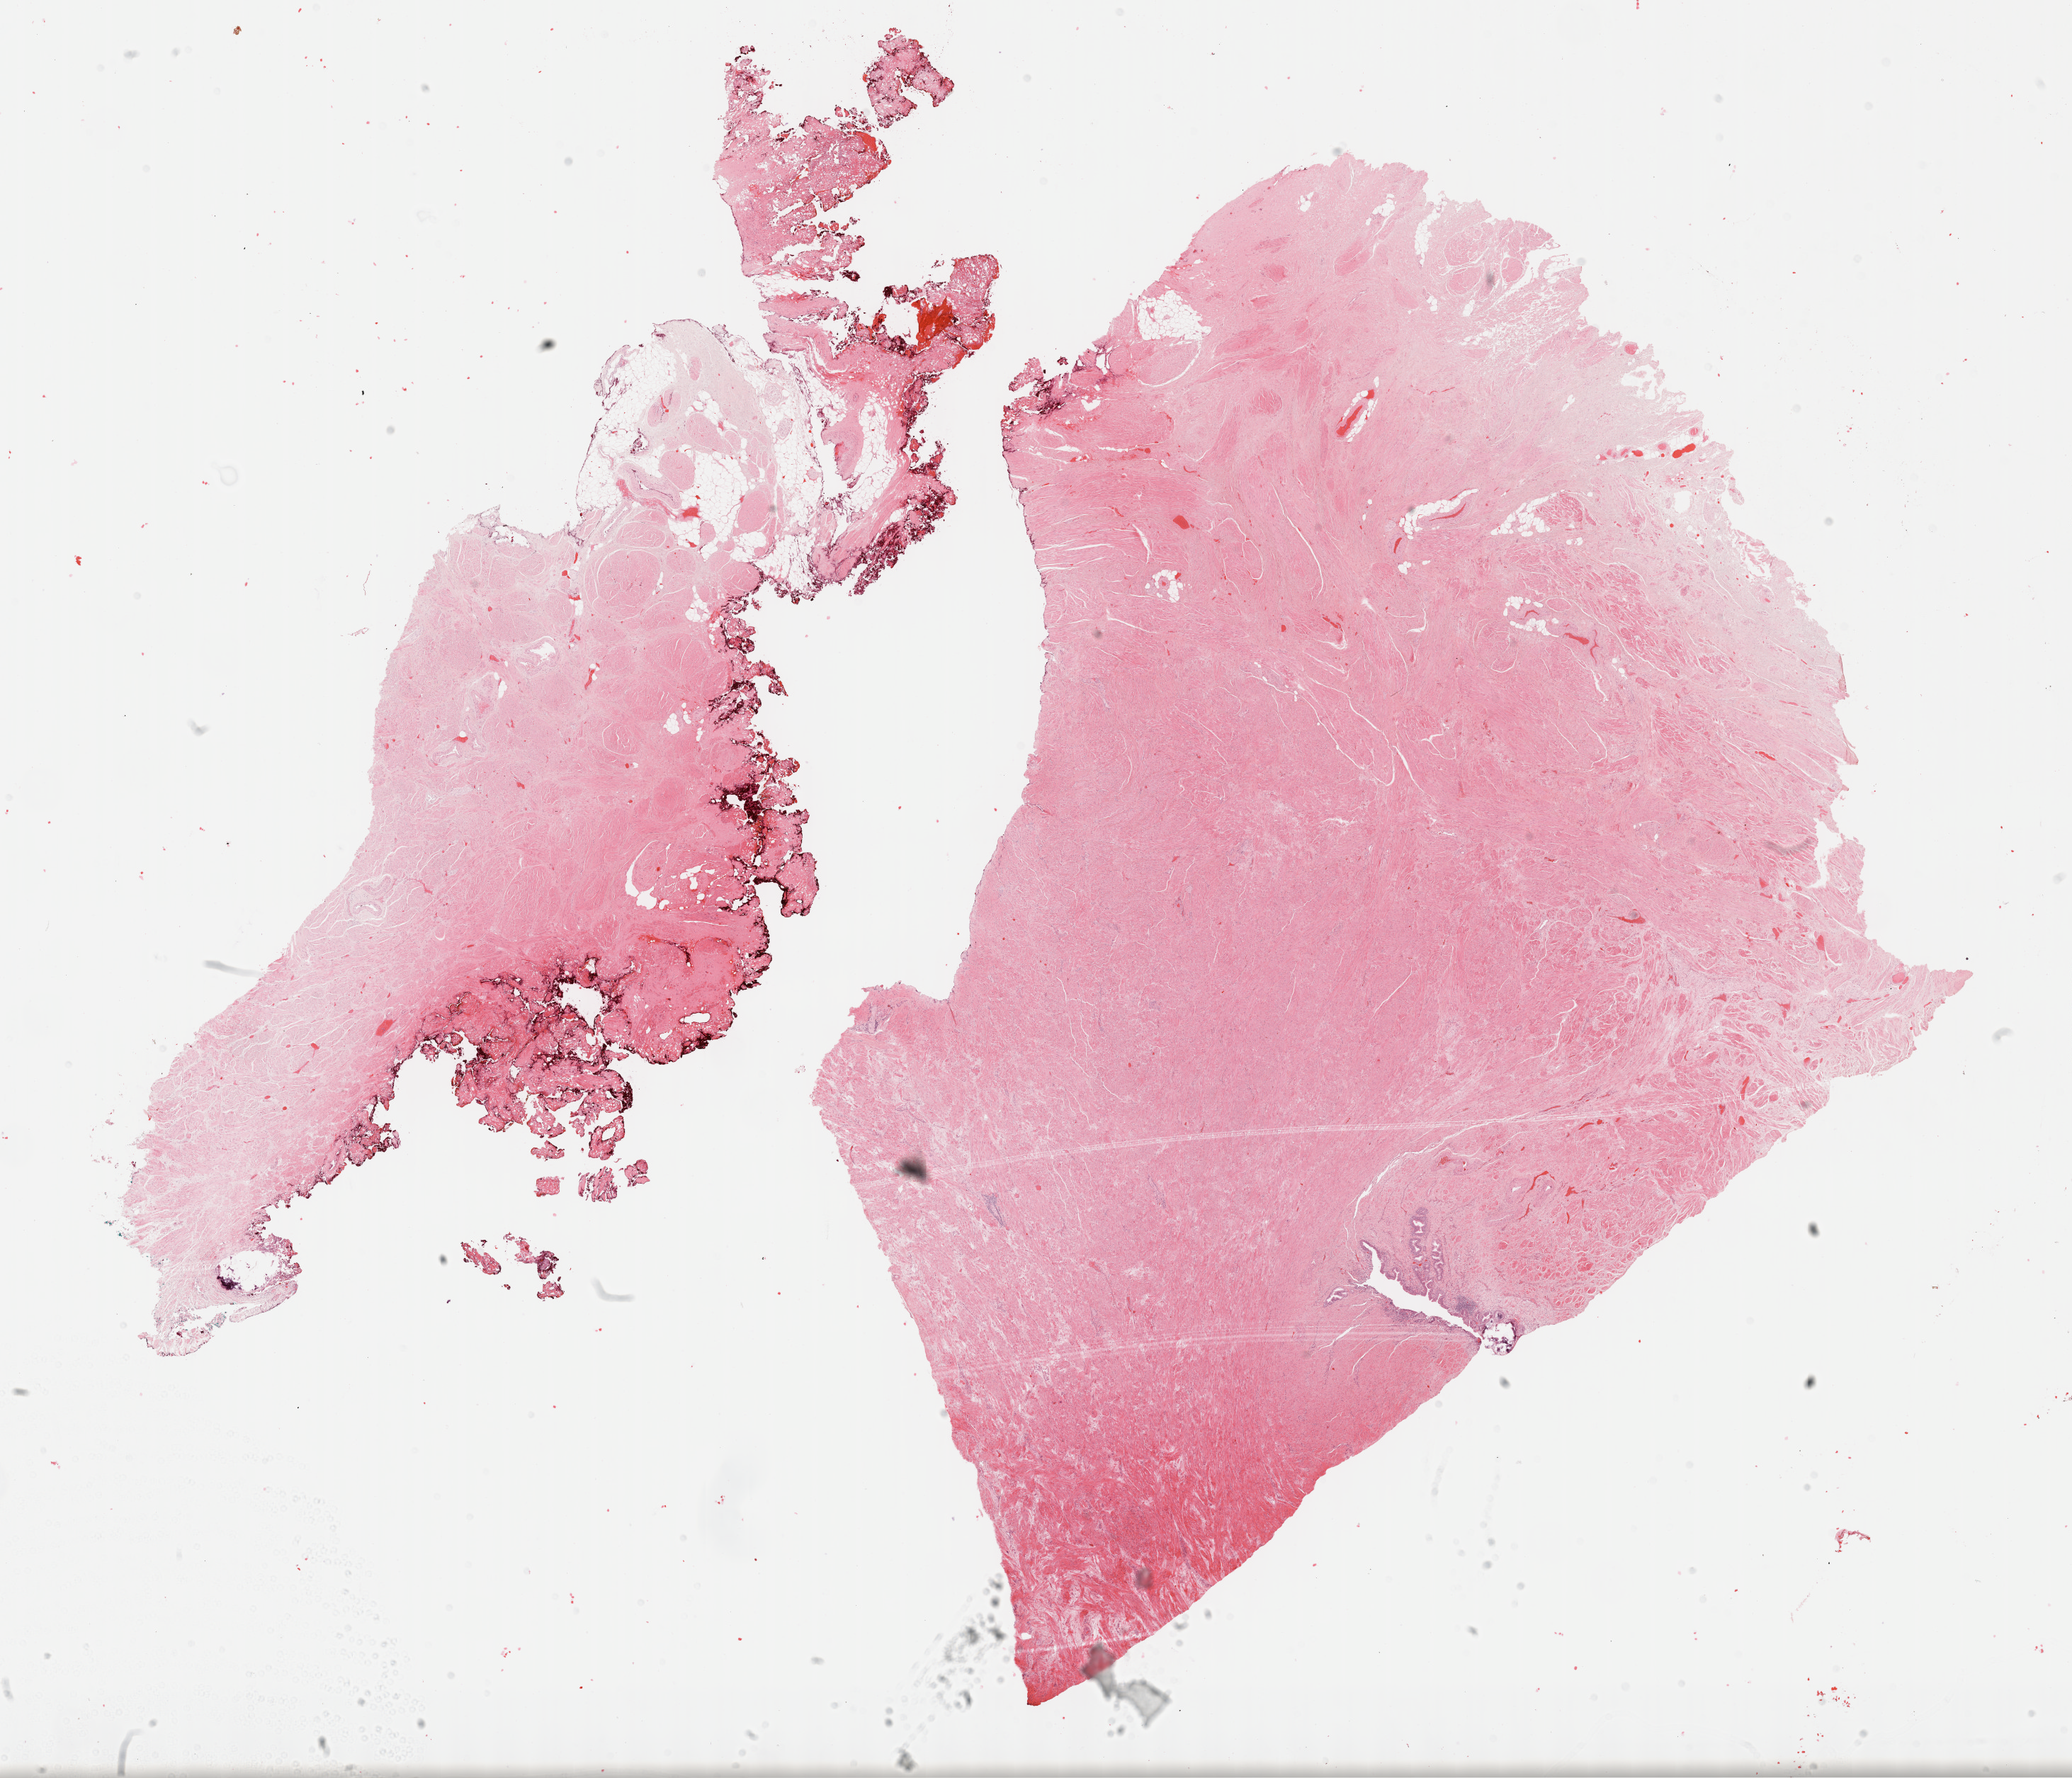
Hematoxylin and eosin (H&E) stained whole-slide image — shown as a low-resolution overview of the whole scanned area (about 23.7 x 20.3 mm), FFPE section, sample: primary tumour, prostate. Male patient; age at initial diagnosis 65 years.
Pathologic diagnosis: Adenocarcinoma, NOS (prostate gland).